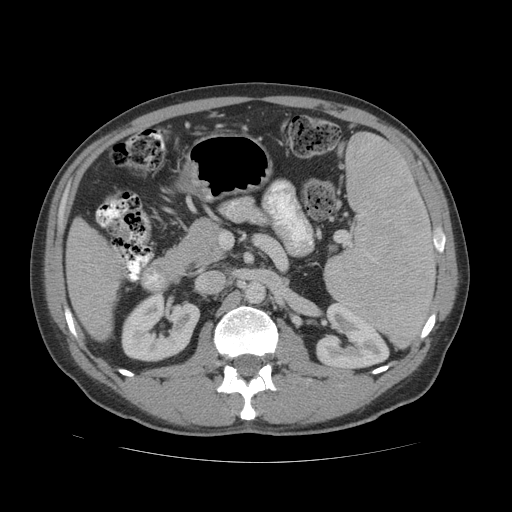
Contrast-enhanced abdominal CT (liver protocol), one axial slice; position 19 of 81 along the scan axis; reconstruction kernel STANDARD; soft-tissue window (W 400 / L 40 HU); 2.5 mm slice thickness; 512 × 512 image matrix, field of view 400 × 400 mm. Case-level facts recorded for this patient, not image findings: diagnosis: hepatocellular carcinoma (patient treated with transarterial chemoembolisation; whether this scan precedes or follows treatment is not stated here); TNM stage (as recorded): Stage-IVB; Child-Pugh class: B; tumour differentiation: well differentiated; tumour nodularity: multinodular.
Outlined on this slice (semi-automatic segmentation, software-assisted and operator-edited):
- liver parenchyma outside the tumour (the mass and vessels are separate outlines, so this box may not span the whole liver): box from (x=66, y=218) to (x=124, y=340) px